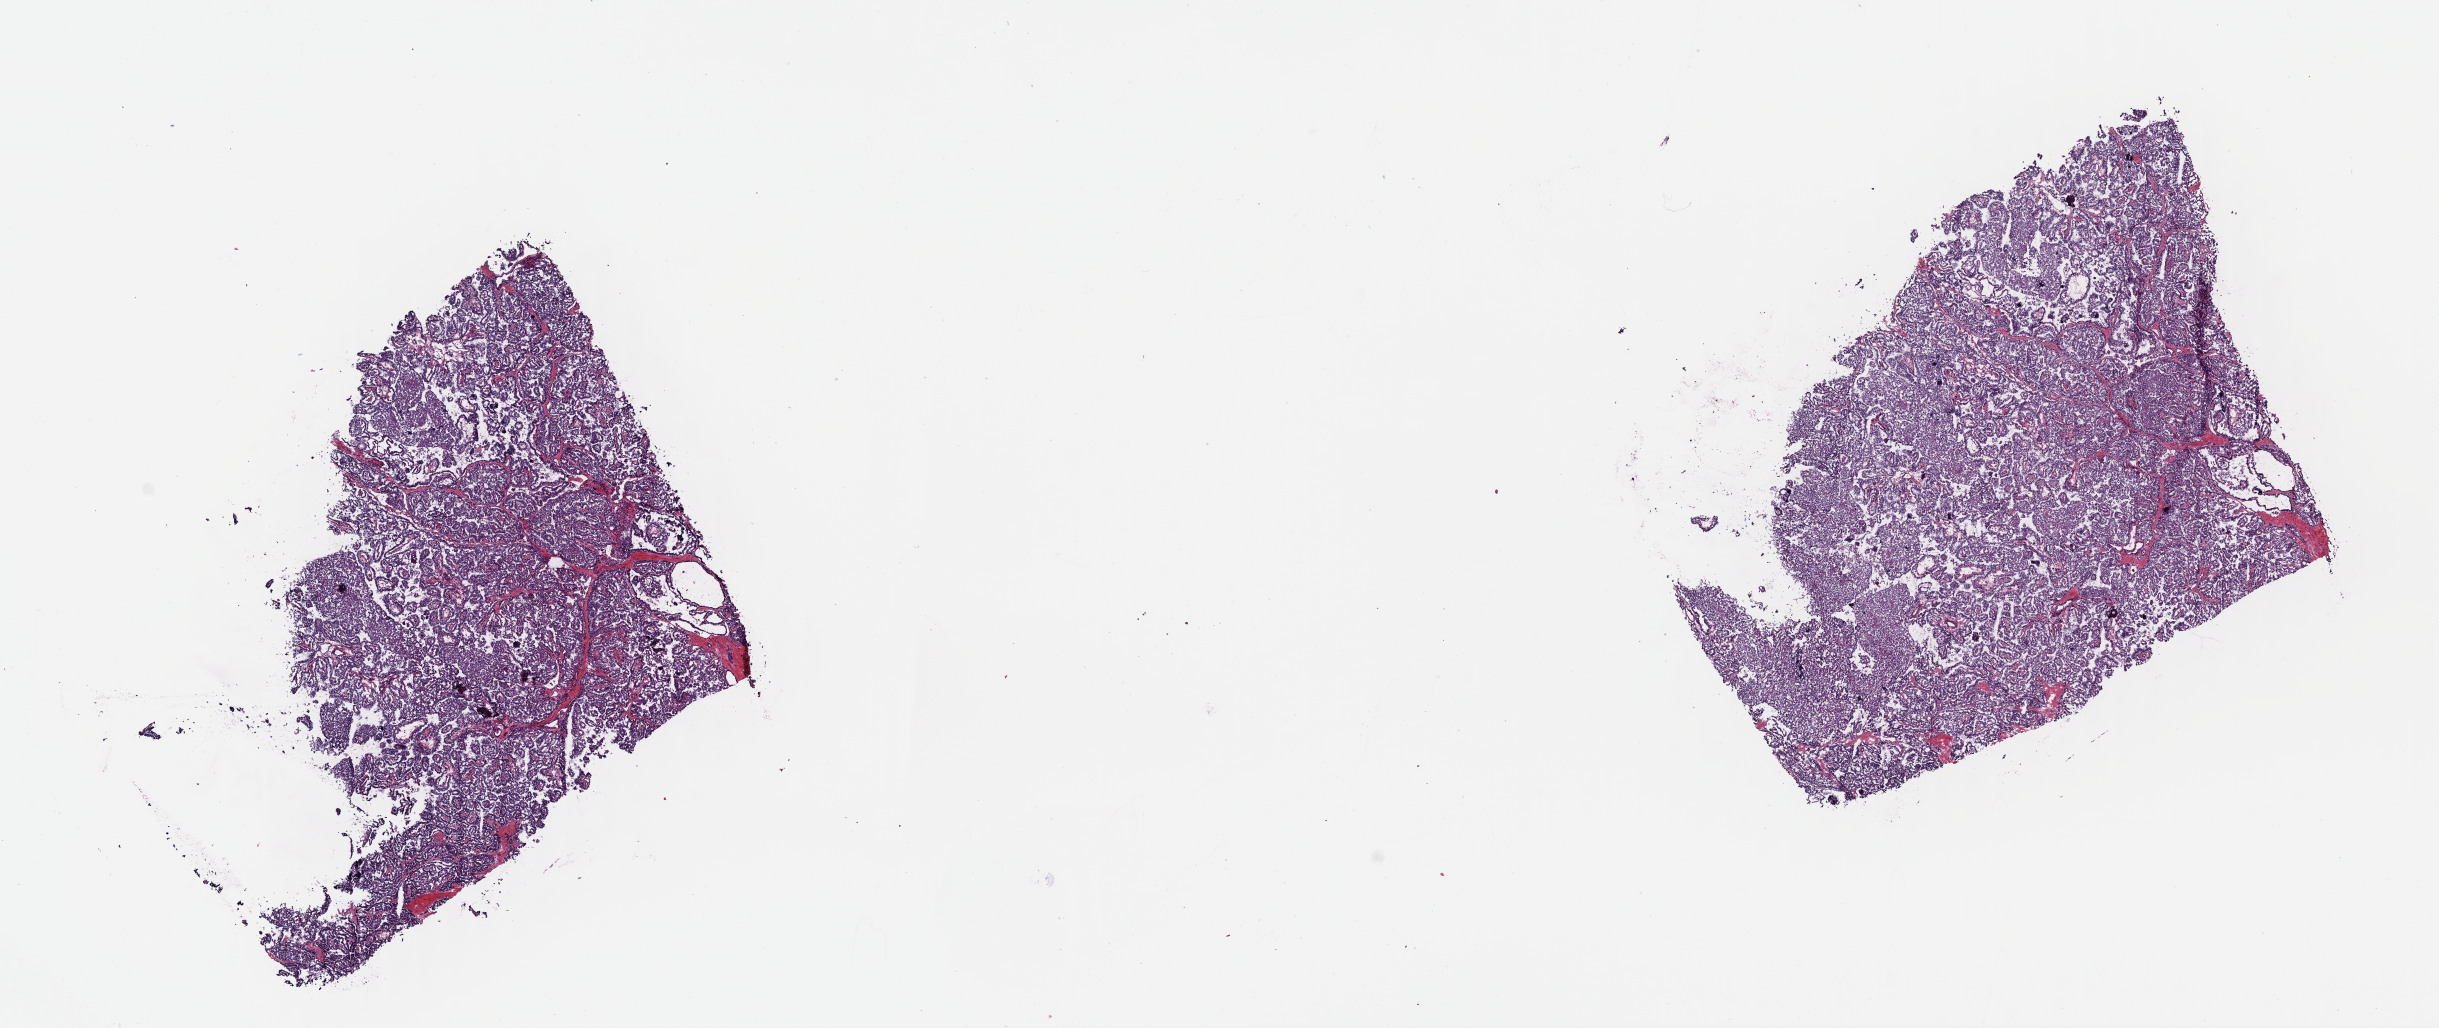
H&E-stained whole-slide image, a low-resolution overview of the entire scanned area, about 19.2 x 8.1 mm. Frozen section. Primary tumour sample from the thyroid. Female patient; age at initial diagnosis 27 years.
Diagnosis: Papillary adenocarcinoma, NOS (thyroid gland).